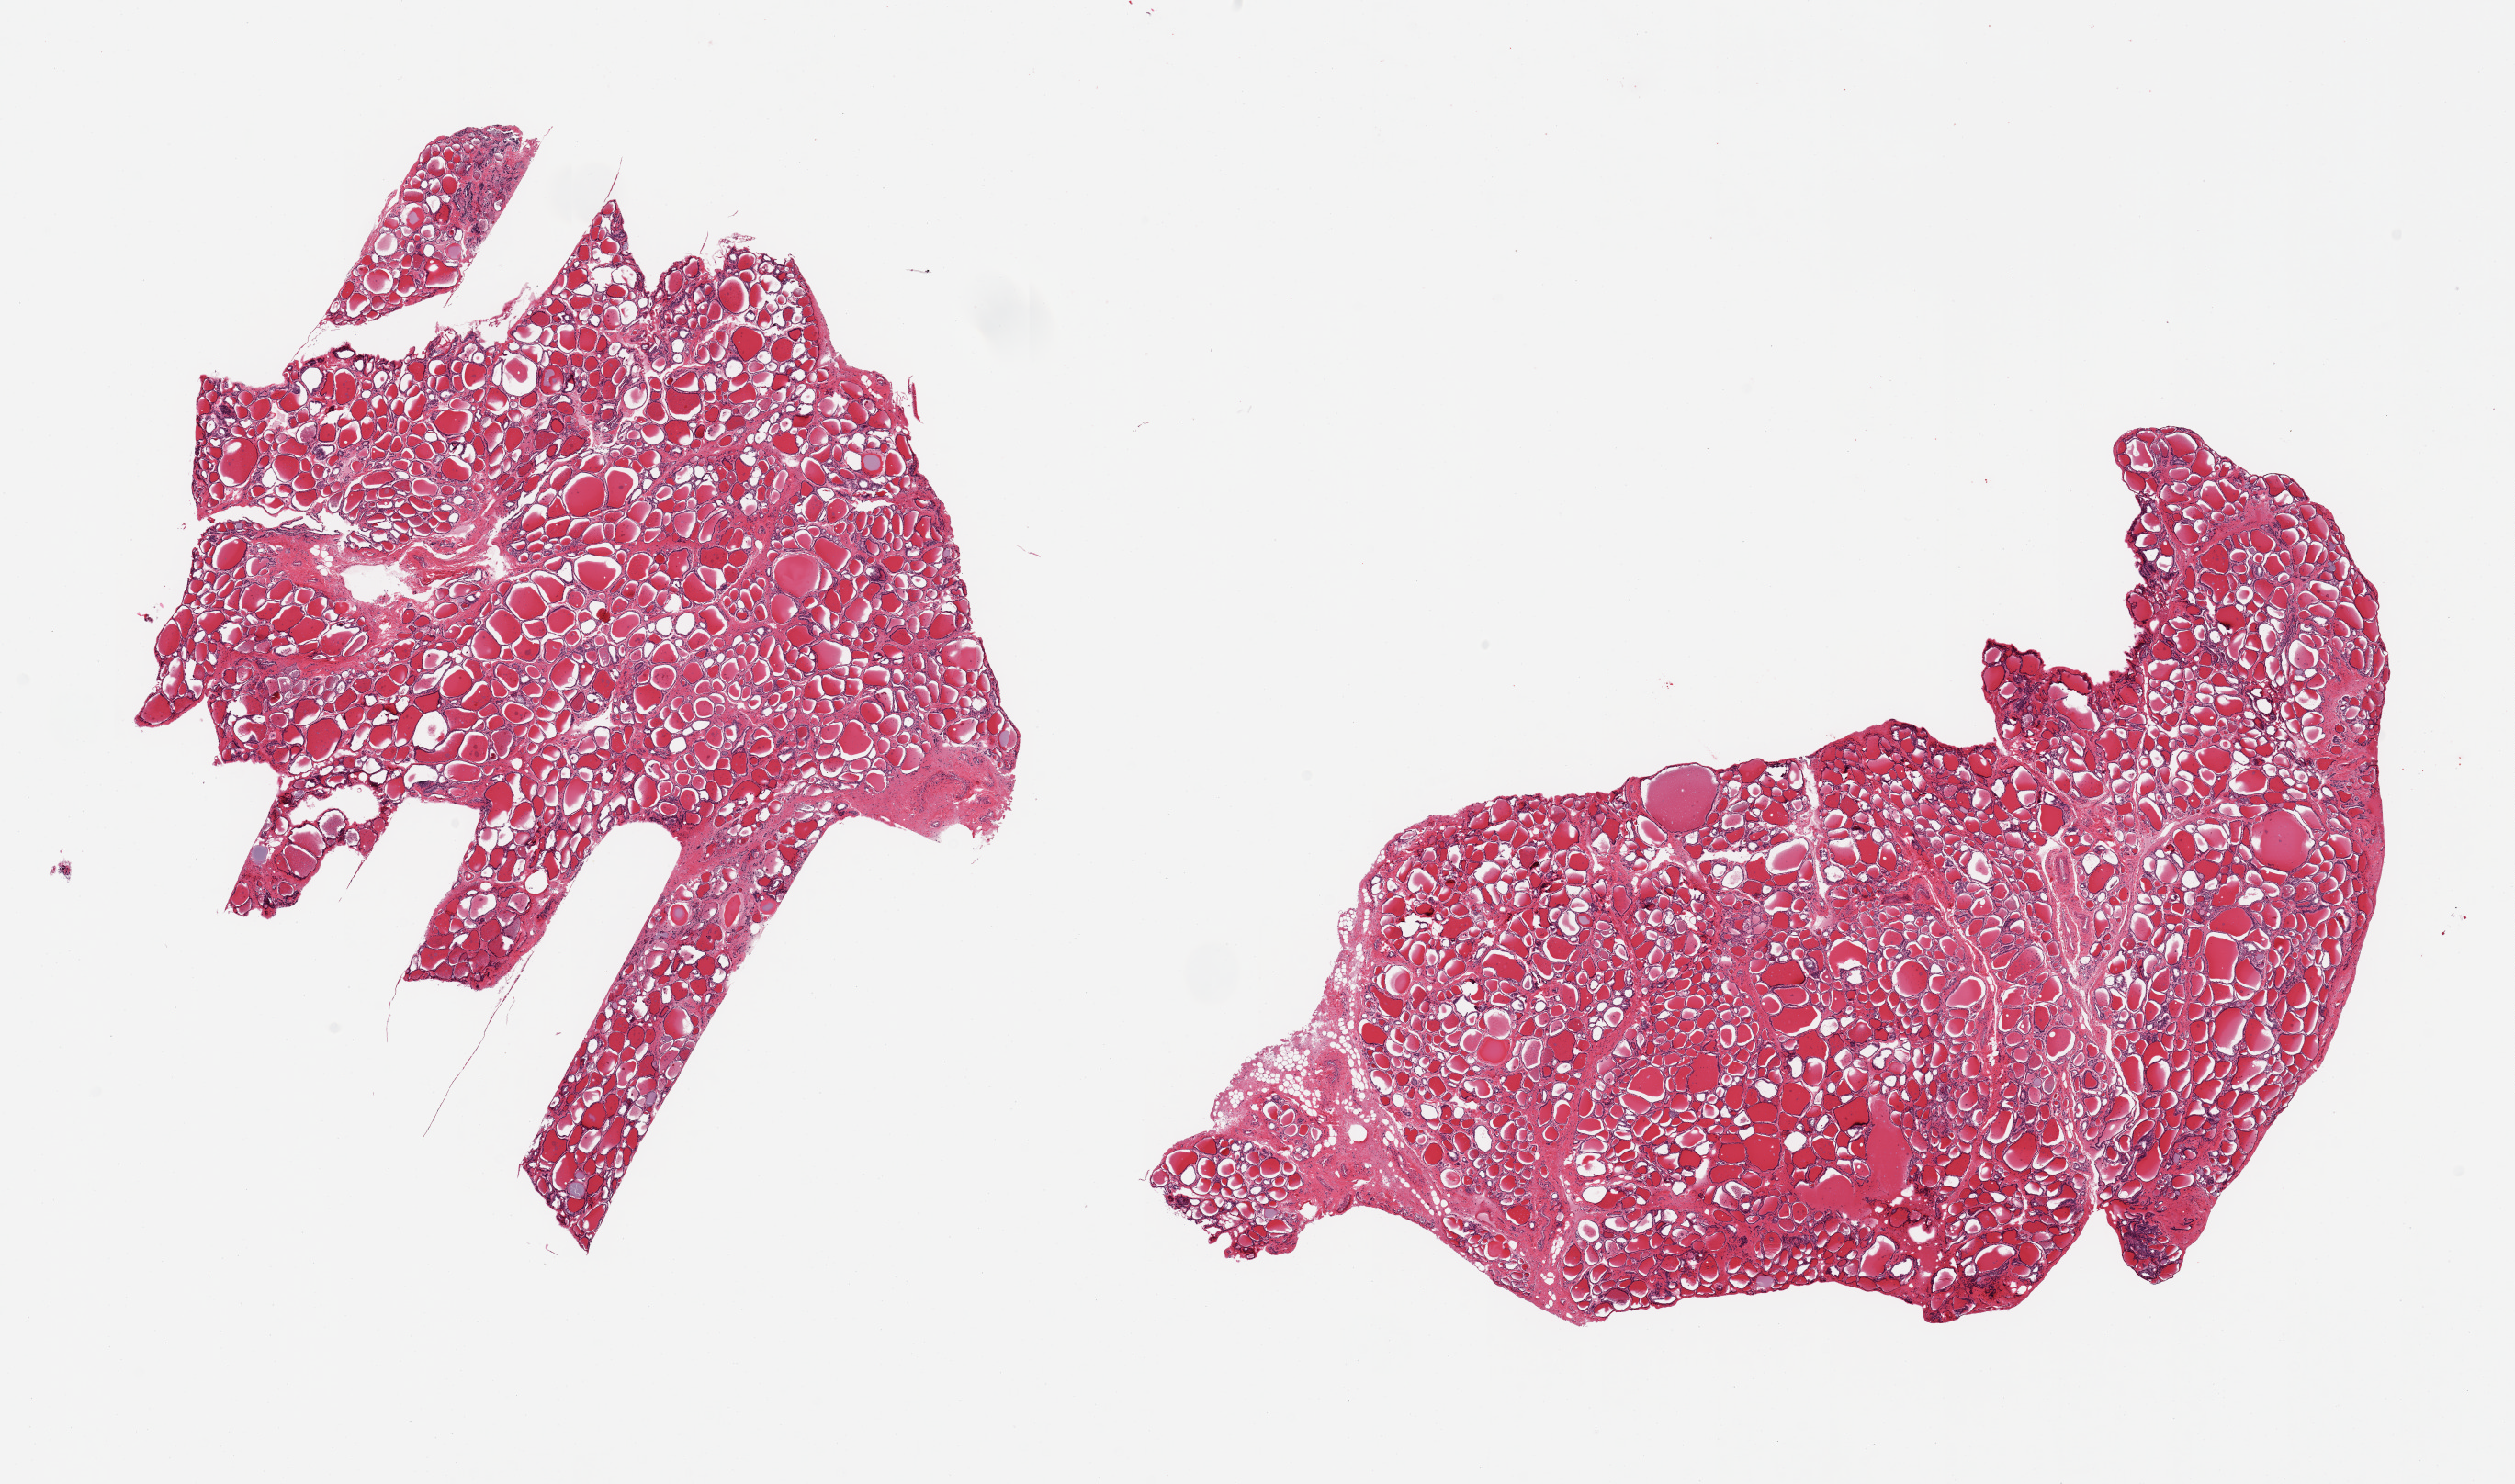
Digitized H&E-stained section — low-resolution overview of the scanned area, about 21.7 x 12.8 mm, PAXgene-fixed paraffin-embedded (PFPE) section, target tissue: thyroid, donor tissue sample. Donor: female.
Pathologist's review note for this sample: 2 pieces, no significant abnormalities.